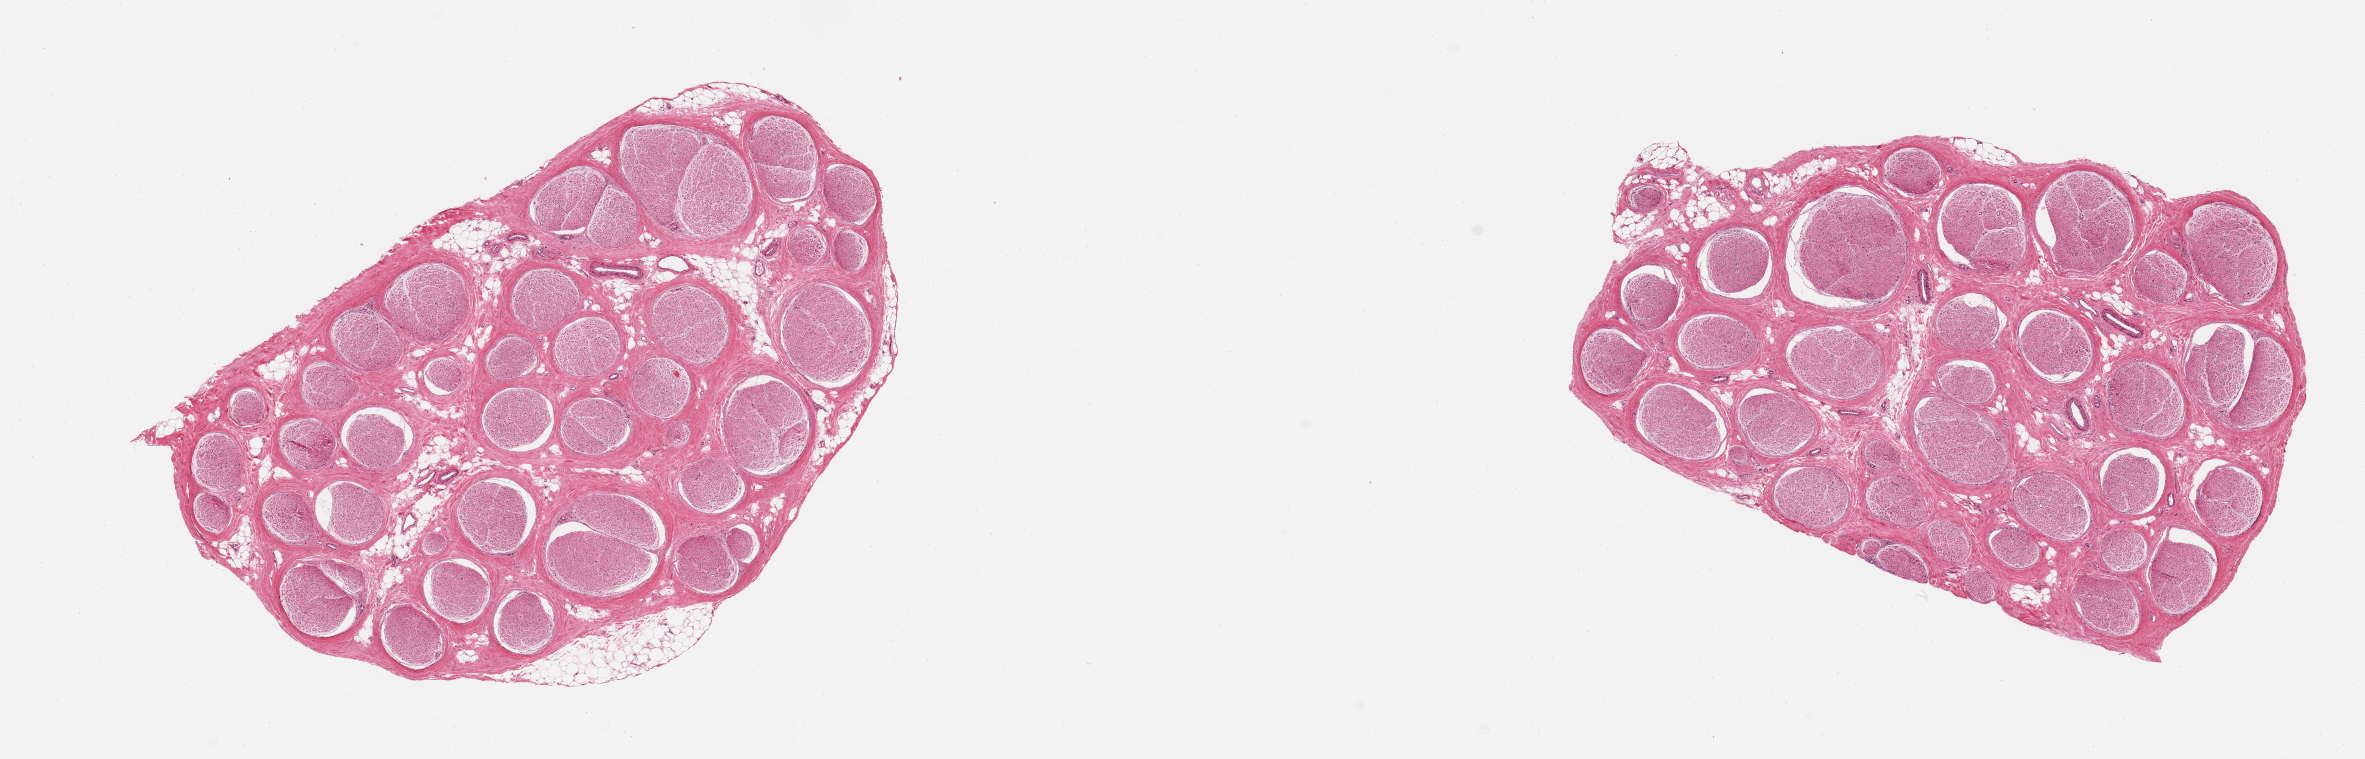
Whole-slide image, hematoxylin and eosin (H&E) stain, low-resolution overview of the scanned area, about 18.7 x 6.0 mm; PAXgene-fixed paraffin-embedded (PFPE) section; section of tibial nerve (target tissue); tissue donor sample. Male donor.
Review note (as recorded): 2 pieces; 5% internal and external fat content.